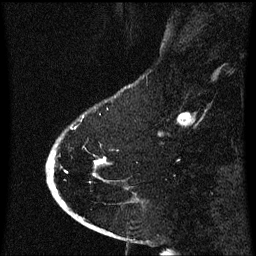
Breast MRI (dynamic contrast-enhanced), one sagittal slice. Slice 13 of 60 in the series (ordered by position). Dynamic contrast-enhanced series, image 2 of 3 at this slice position (ordered by acquisition). 1.5 T. TE 4.2 ms, TR 8.4 ms. 2.1 mm slice thickness. 256 × 256 image matrix, field of view 200 × 200 mm. Patient: female, 53 years. From the clinical record (not read from this slice): setting: breast cancer imaged before/during neoadjuvant chemotherapy; receptor status: HR-positive, HER2-negative.
Structures marked on this image (semi-automatic segmentation, software-assisted and operator-edited):
- analysis volume of interest (the breast-tissue region the enhancement analysis was run in; not a lesion): box from (x=49, y=140) to (x=108, y=201) px
- tumour enhancement mask (voxels above the 70 % enhancement threshold inside the analysis volume of interest): (x=96, y=158)–(x=106, y=165)